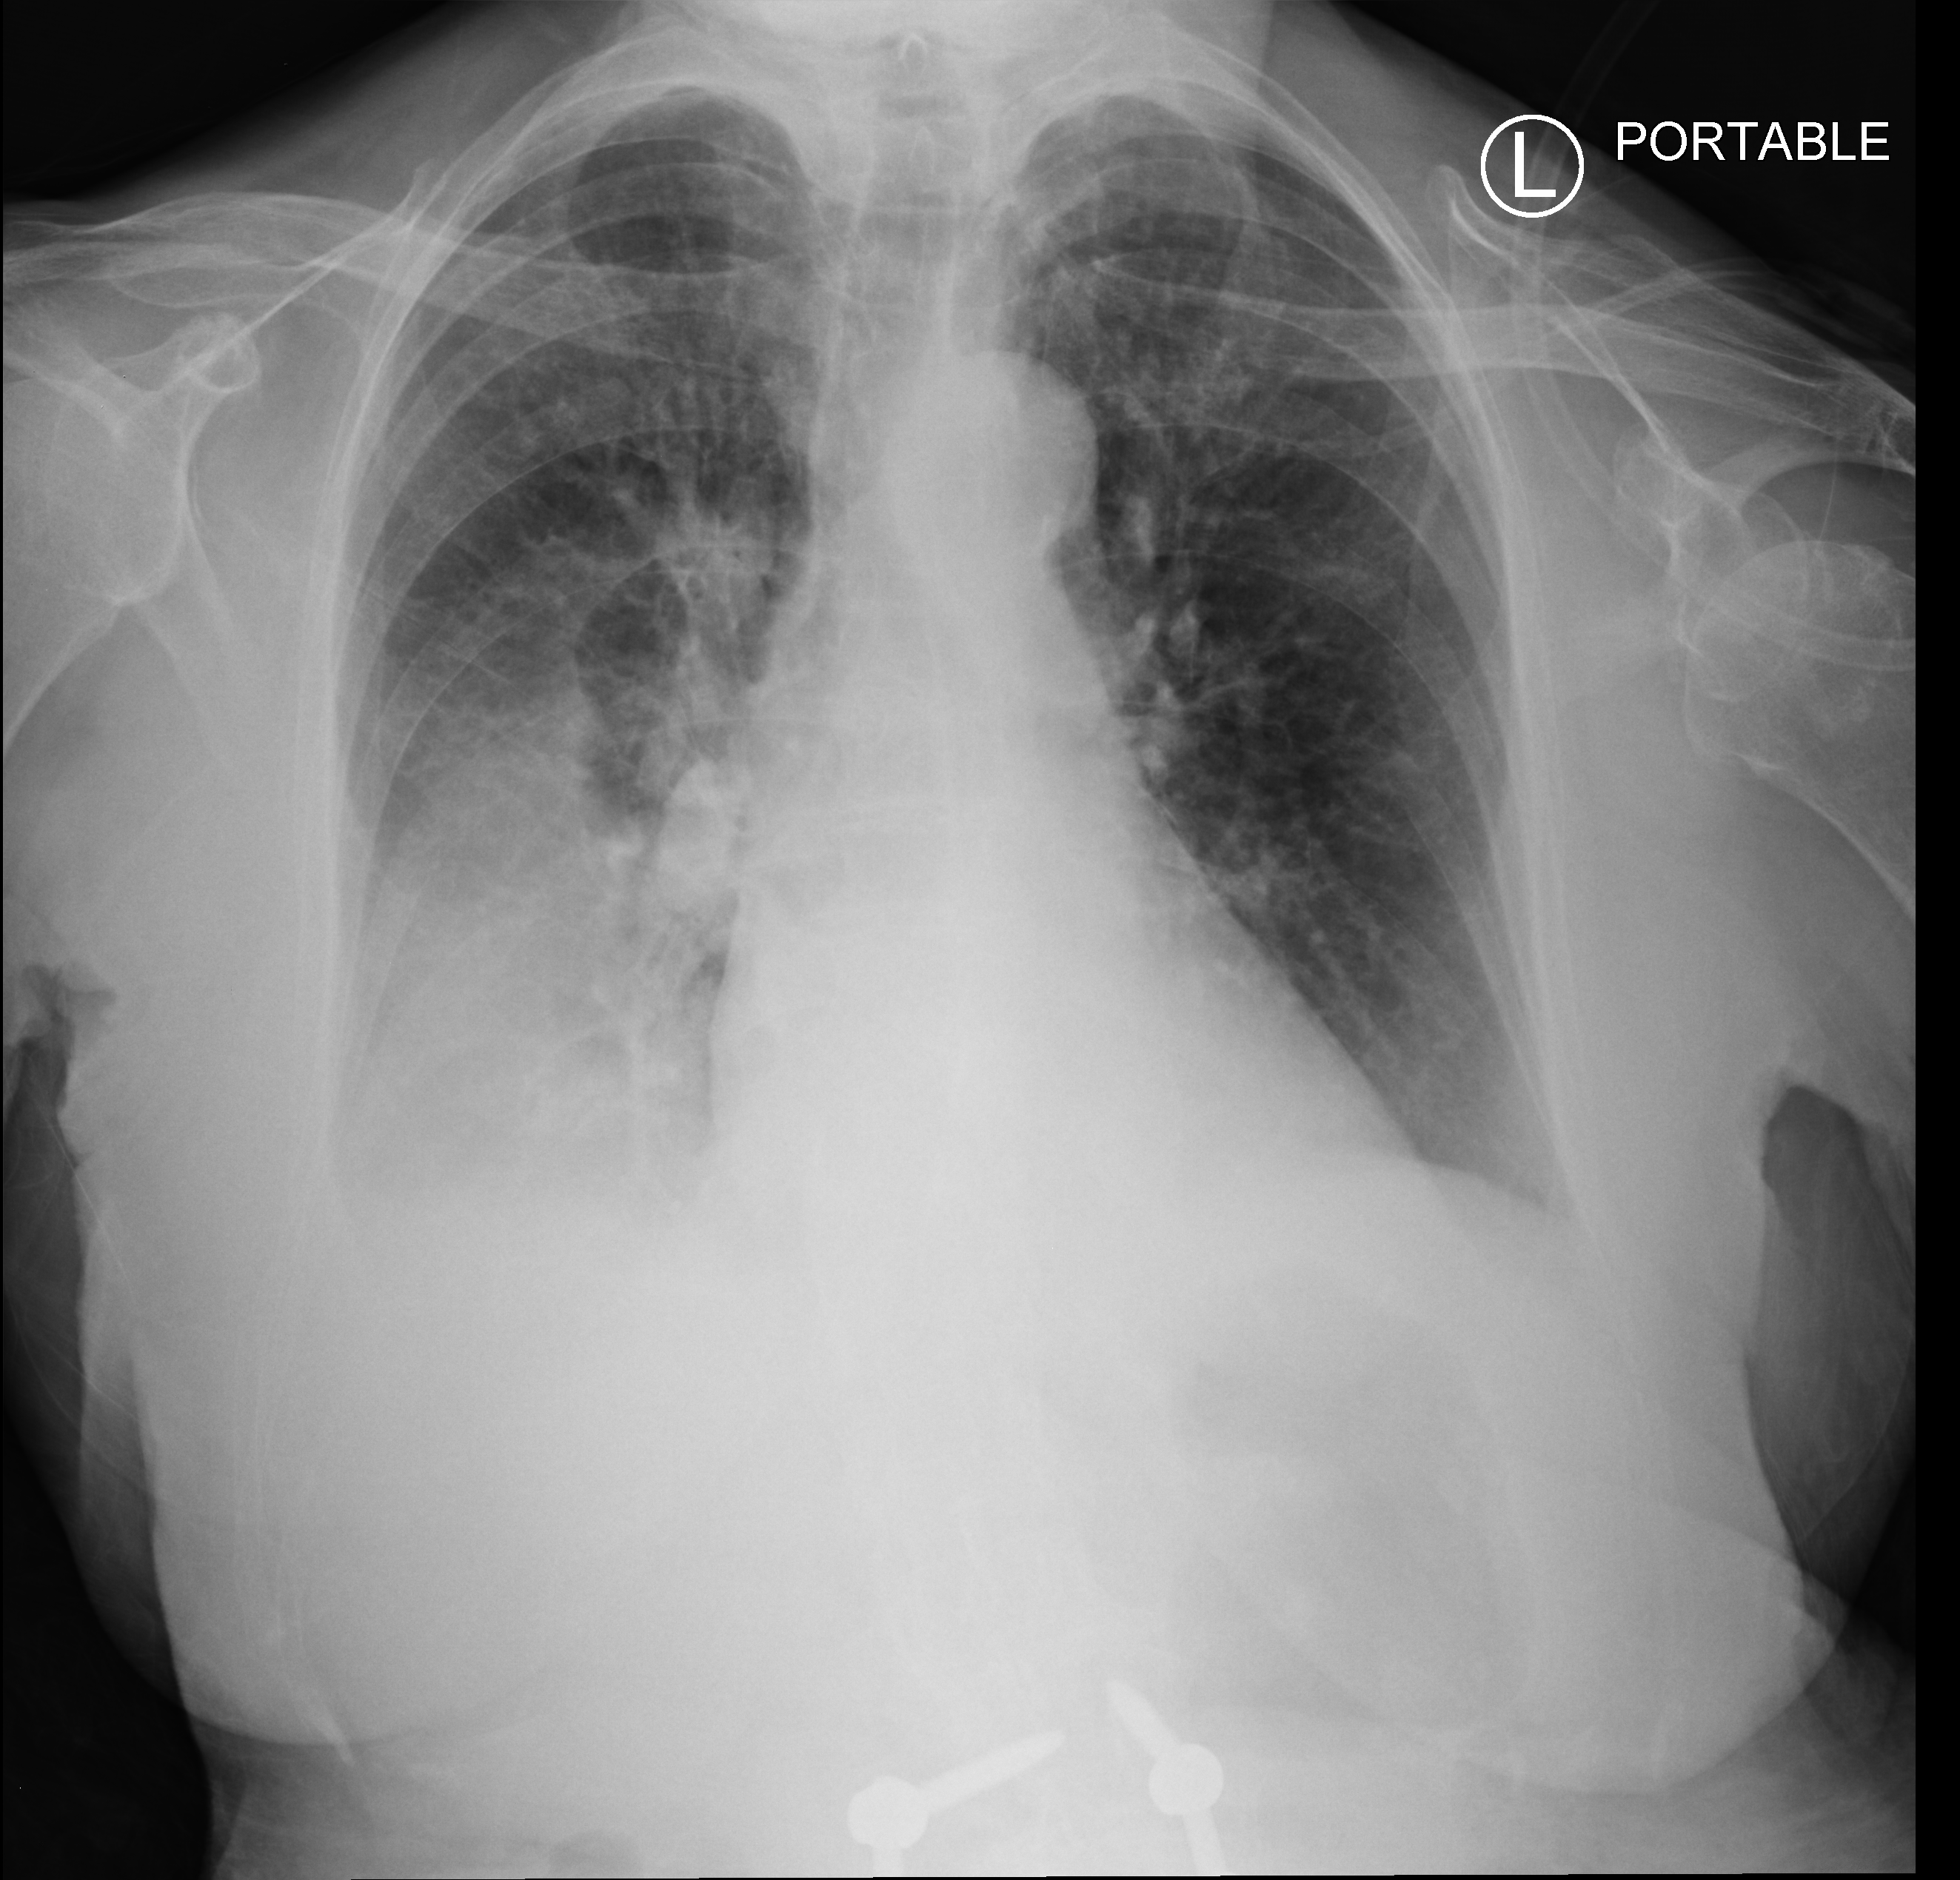
Portable chest radiograph; anteroposterior (AP) projection. Patient hospitalised with COVID-19; female, aged 60–74 years.
From the hospital-stay record, not from the radiograph (when in the stay this image was taken is not recorded): admitted to intensive care during this hospital stay: no; mechanically ventilated during this hospital stay: no.